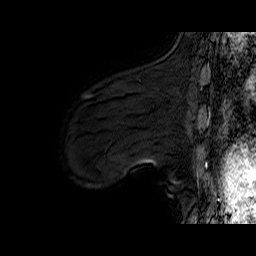
Breast MRI (dynamic contrast-enhanced), one sagittal slice; slice 14 of 60 in the series (ordered by position); dynamic contrast-enhanced series, time point 2 of 6 at this slice position (early post-contrast); 1.5 T; TE 6.4 ms, TR 32.9 ms; 256 × 256 image matrix, field of view 200 × 200 mm. Female patient. From the clinical record (not read from this slice): setting: breast cancer imaged before/during neoadjuvant chemotherapy; receptor status: HER2-positive.
Structures marked on this image (semi-automatically segmented with operator editing):
- analysis volume of interest (the breast-tissue region the enhancement analysis was run in; not a lesion): bounding box <78,94,152,149> (left, top, right, bottom; pixels)
- tumour enhancement mask (voxels above the 100 % enhancement threshold inside the analysis volume of interest): <86,95,91,98>